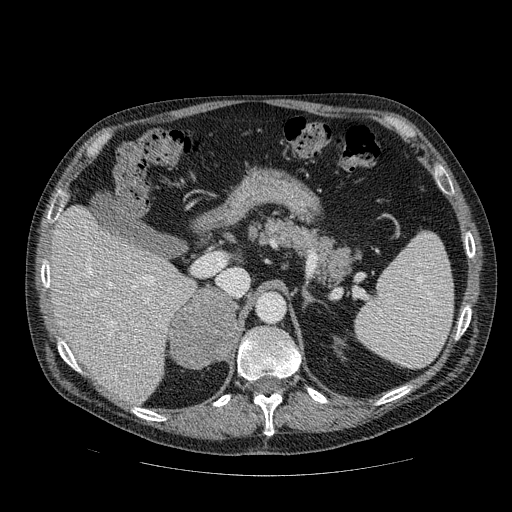
Contrast-enhanced abdominal CT, one axial slice; position 60 of 111 along the scan axis; reconstruction kernel STANDARD; 120 kVp; intravenous contrast given; soft-tissue window (W 400 / L 40 HU); 2.5 mm slice thickness; 512 × 512 image matrix, field of view 420 × 420 mm. Male patient, age 56 years. From the clinical record (not read from this slice): diagnosis: adrenocortical carcinoma; tumour side: right adrenal; tumour size at pathology: 9 cm; Ki-67 index: 48 %; stage (as recorded): 4.
Outlined on this slice (semi-automatic segmentation, software-assisted and operator-edited):
- mass: bounding box (x1, y1, x2, y2) in pixels: (169, 286, 237, 368)